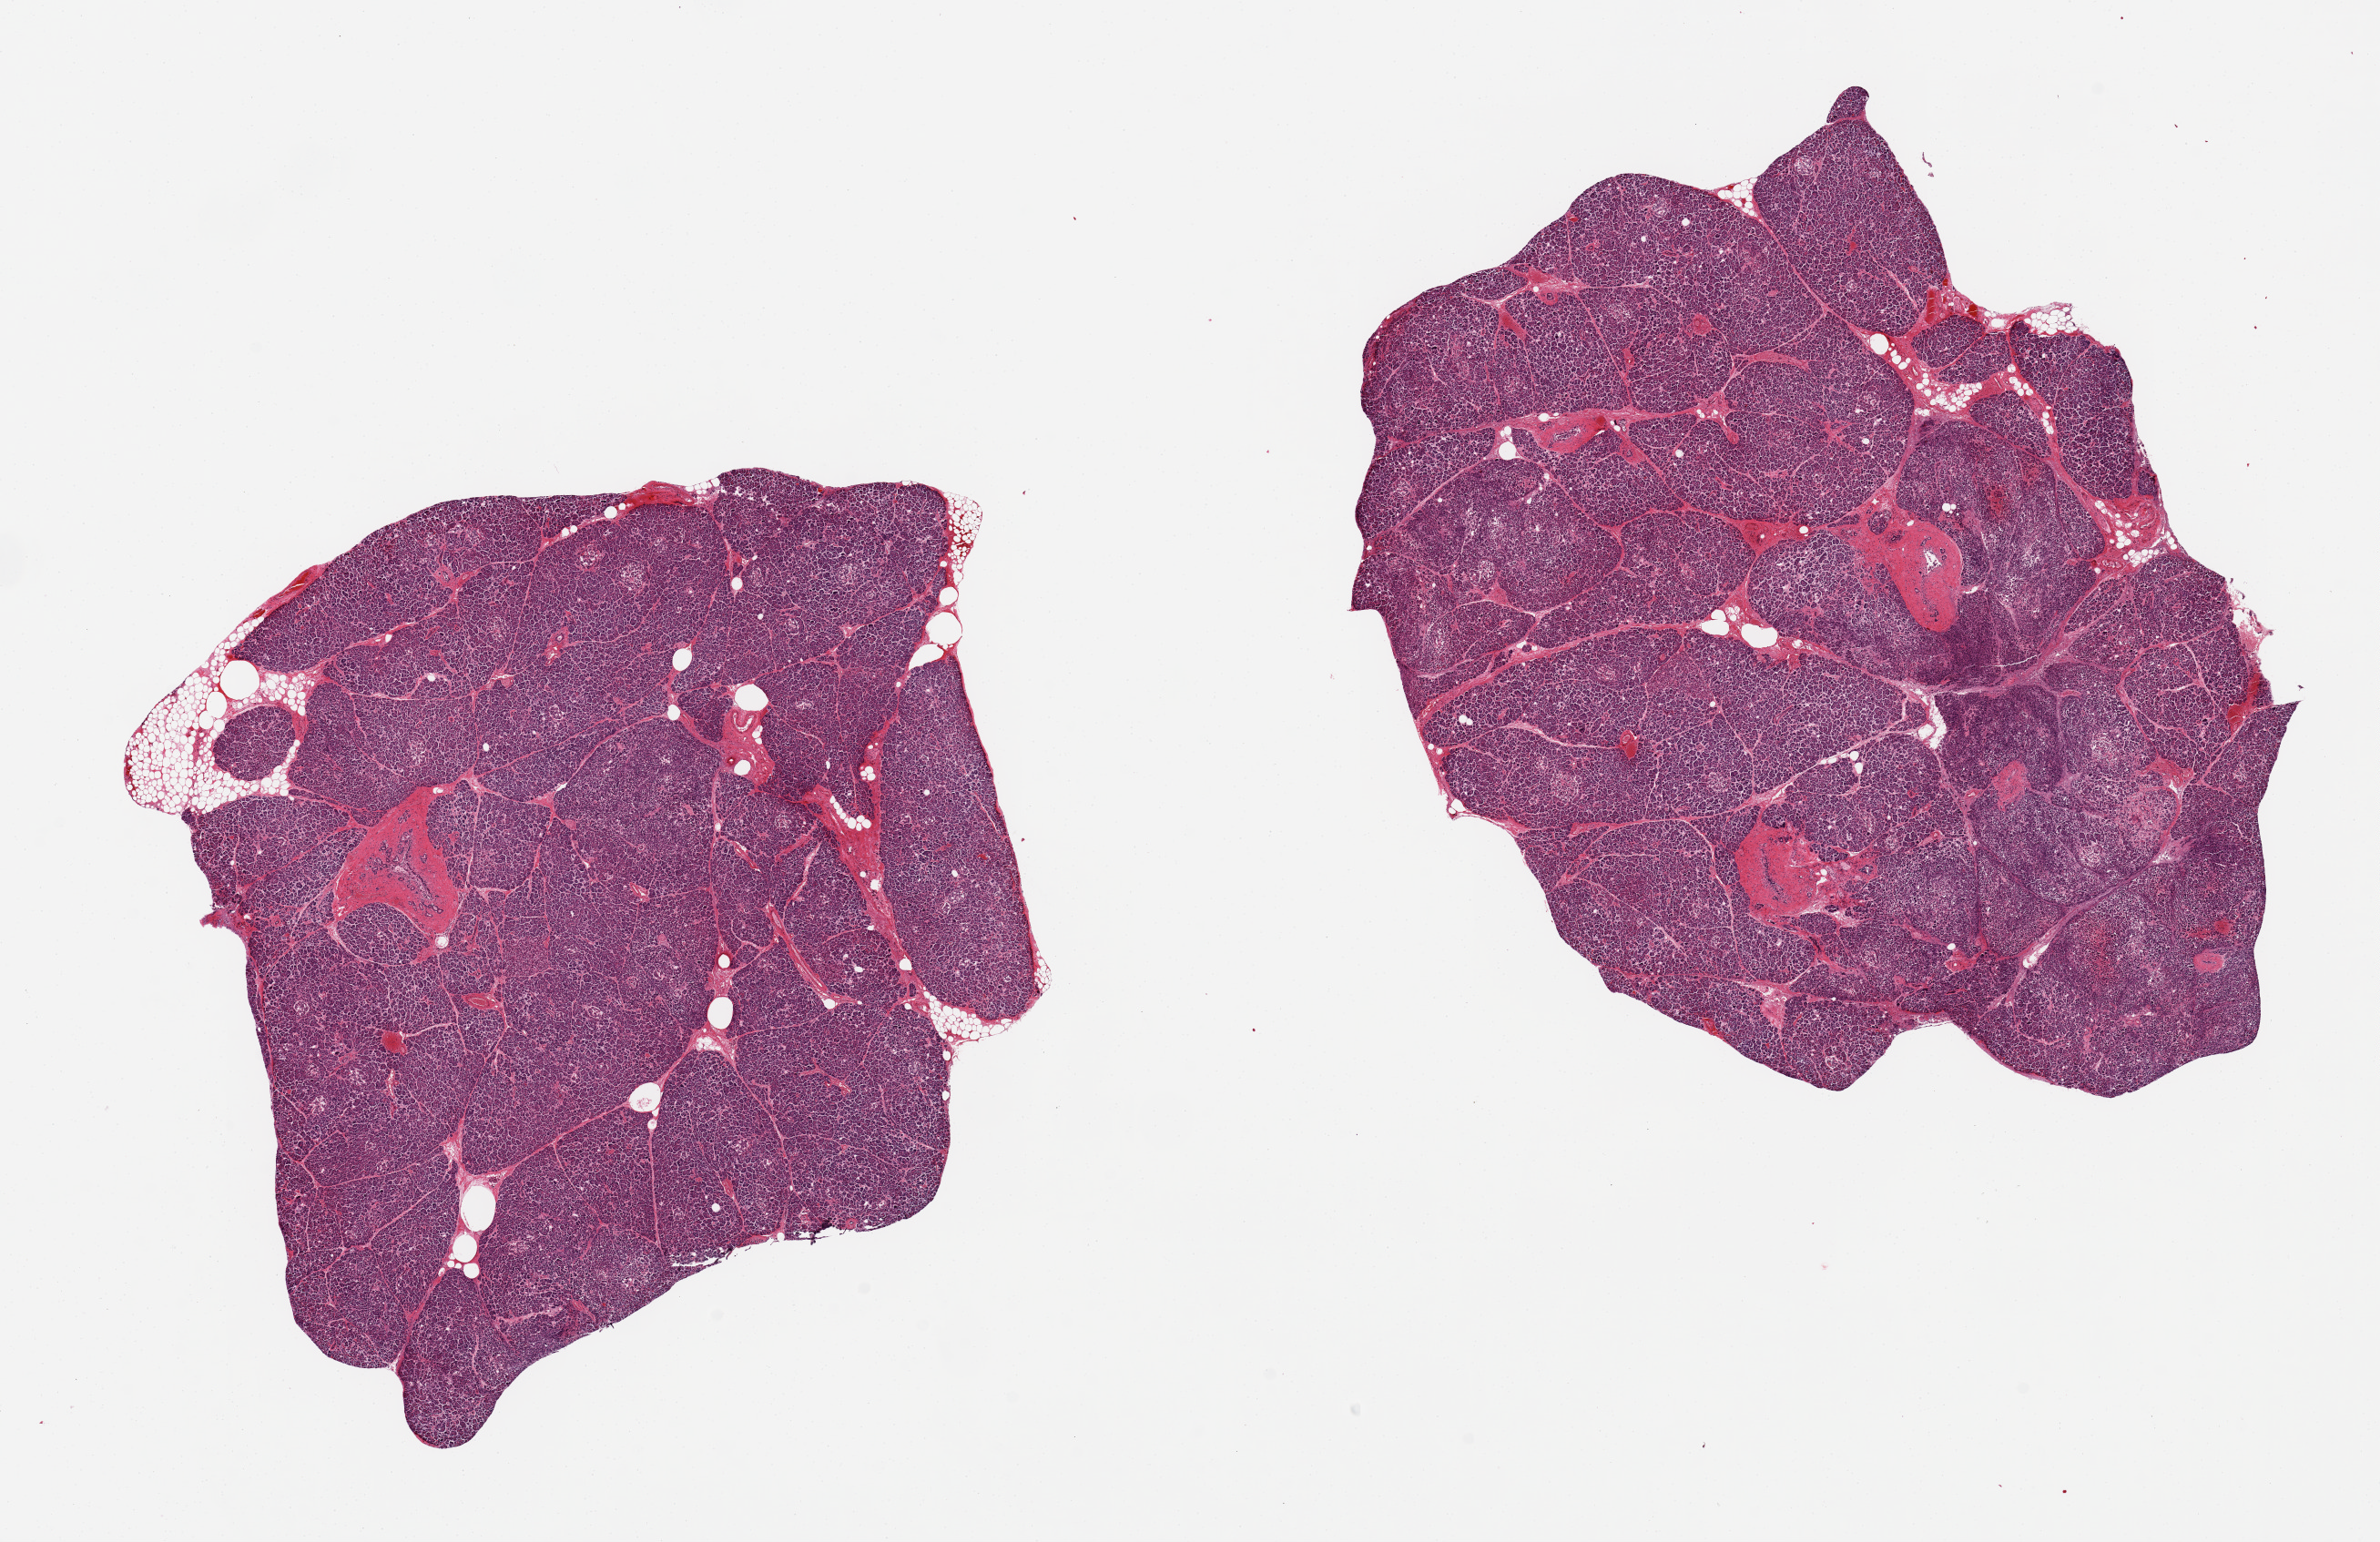
H&E whole-slide image, shown as a low-resolution overview of the whole scanned area (about 20.7 x 13.4 mm, acquisition: 20x scan); PAXgene-fixed paraffin-embedded (PFPE) section; target tissue: pancreas; donor tissue sample. Male donor.
Pathologist's review note for this sample: 2 pieces, 8x8 & 9x7mm; moderate saponification, some Islets visible.